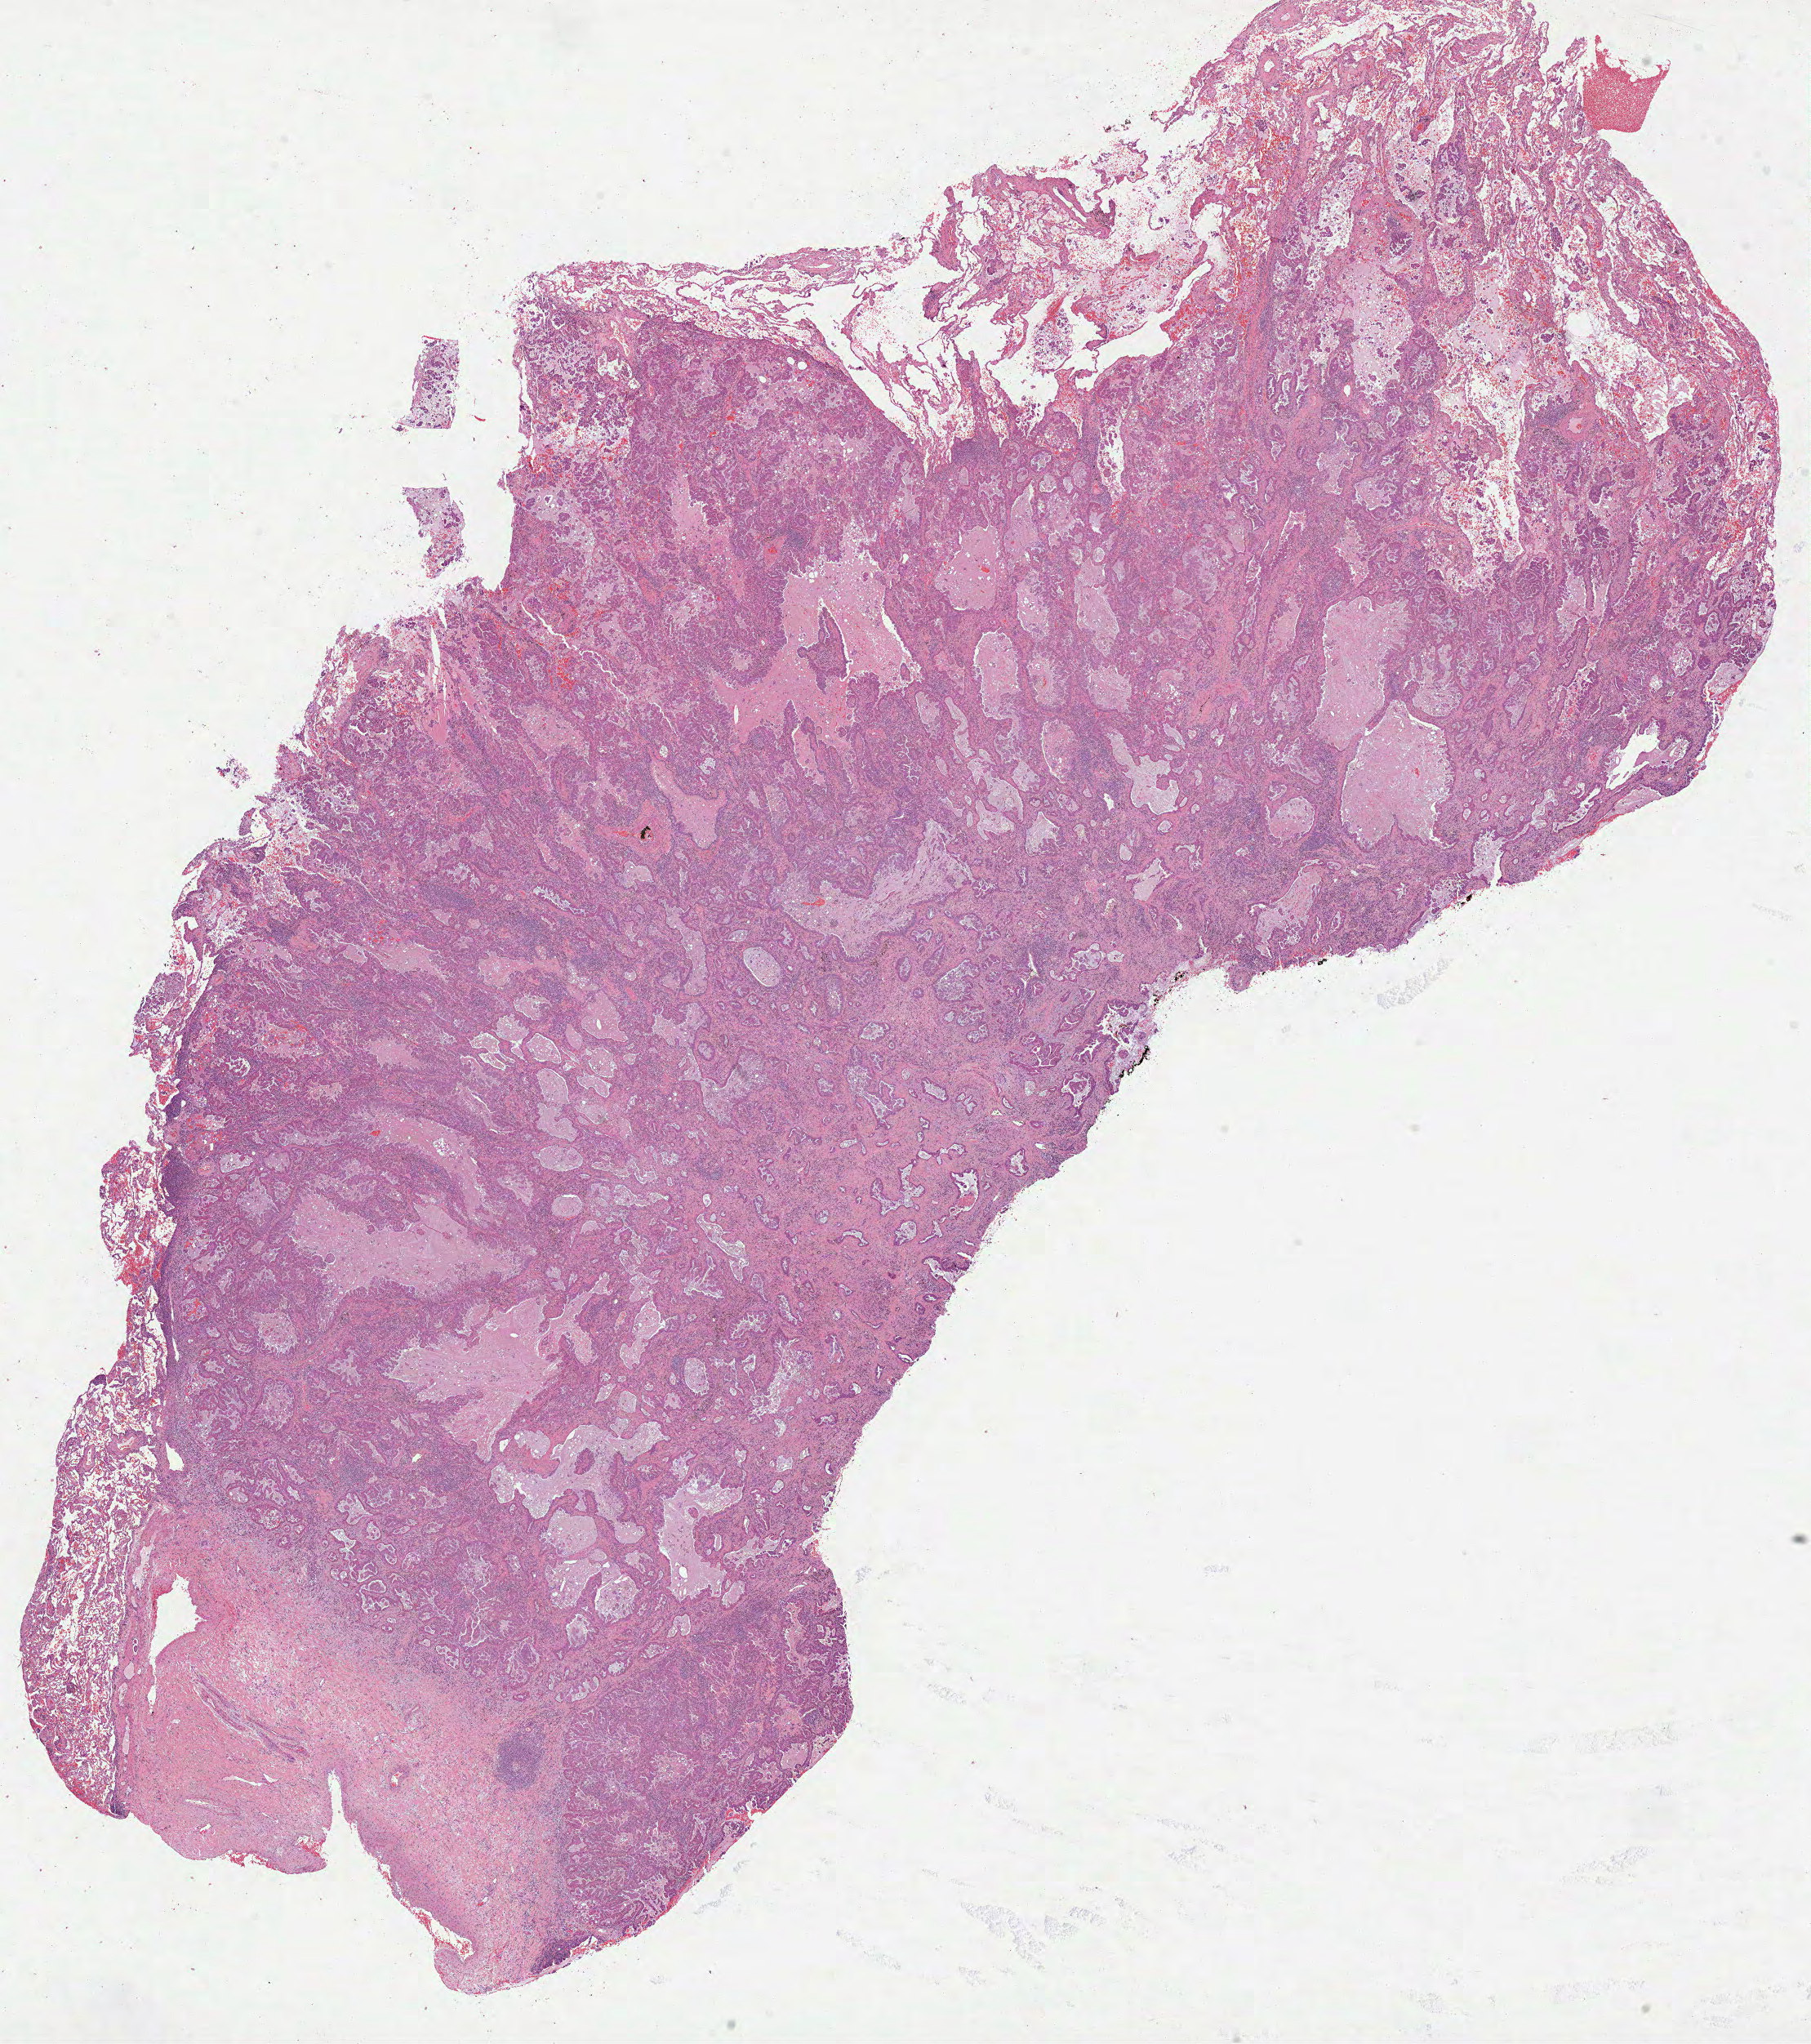
Digitized Hematoxylin and eosin (H&E) stained tissue section (whole slide) — low-resolution overview of the scanned area, about 17.9 x 20.2 mm (slide scanned at 40x). FFPE section. Primary tumour sample from the lung. Female, age 67 years at initial diagnosis.
Diagnosis: Papillary adenocarcinoma, NOS (upper lobe, lung).